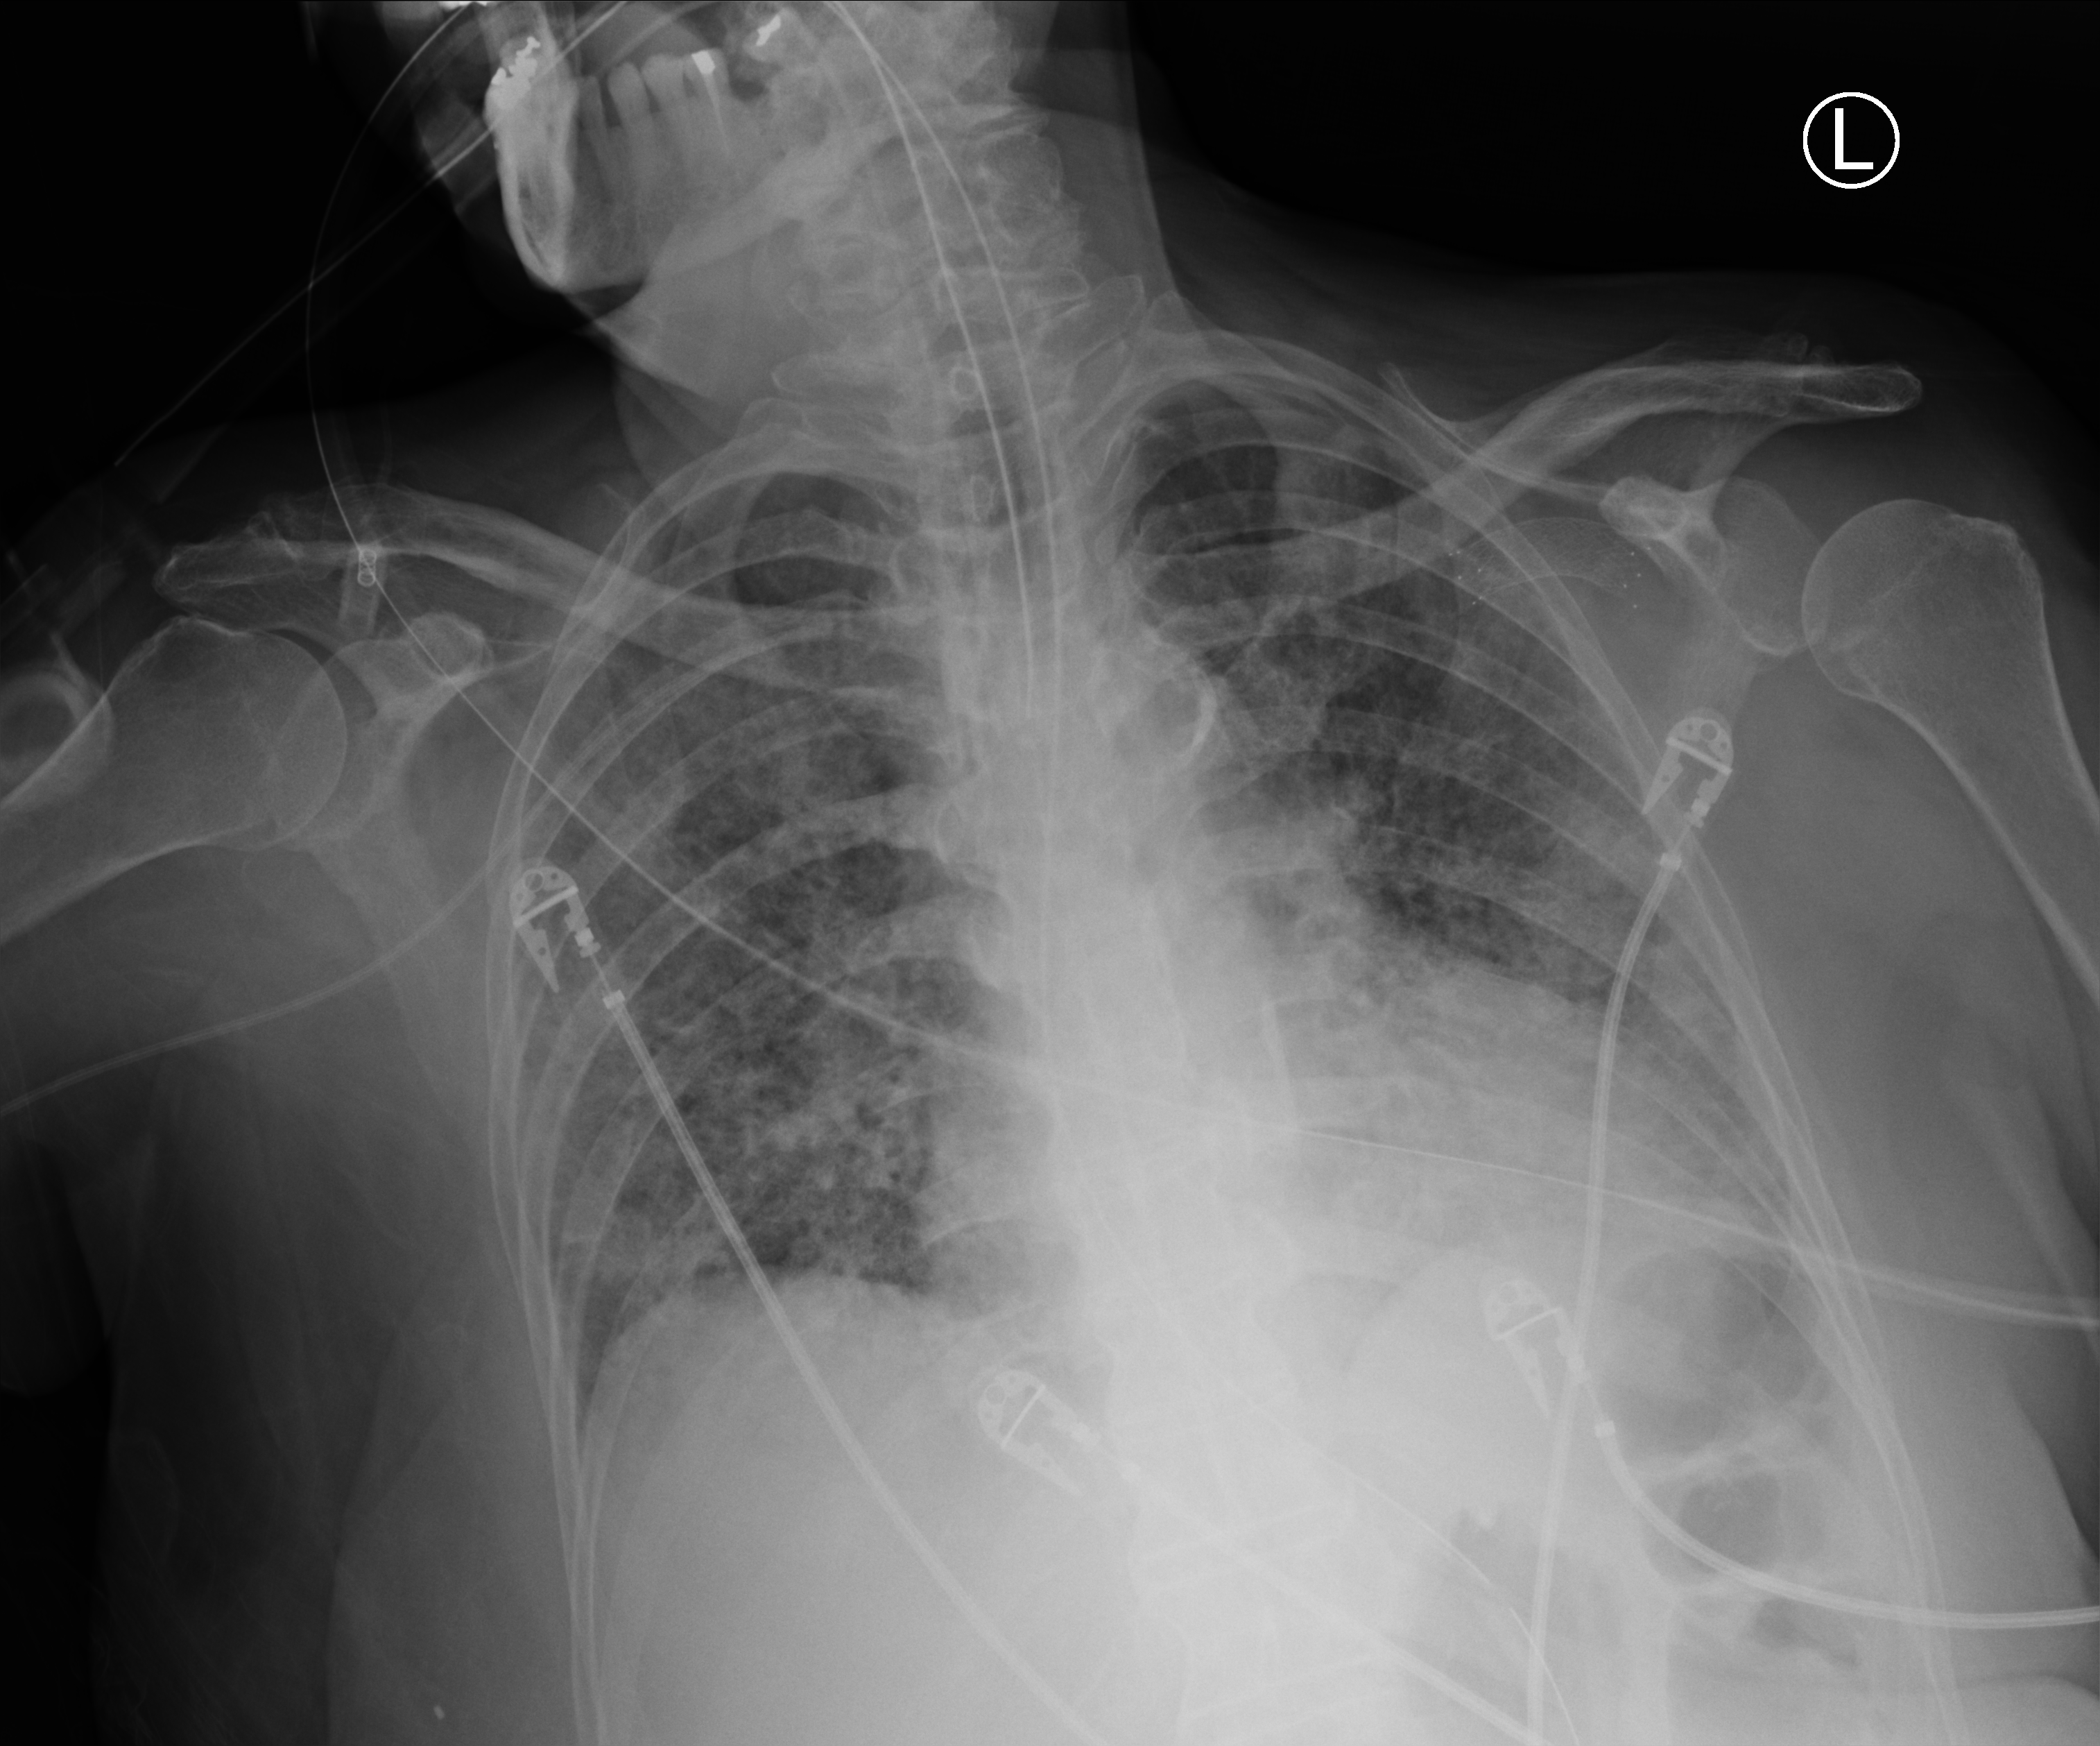
Chest X-ray (portable). Patient hospitalised with COVID-19; female, aged 60–74 years.
Admission-level facts for this patient (not findings on this image; timing relative to this image not recorded):
- mechanically ventilated during this hospital stay: yes